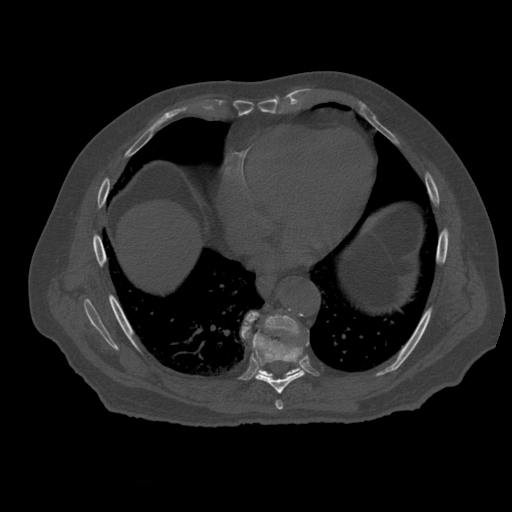
CT including the spine, one axial slice. Slice 335 of 399 in the series (ordered by position). Reconstruction kernel STANDARD. 120 kVp. Bone window (W 1800 / L 400 HU). 1.25 mm slice thickness. 512 × 512 image matrix, field of view 407 × 407 mm. Patient age 73 years. From the clinical record (not read from this slice): primary cancer: prostate.
Structures marked on this image (semi-automatic segmentation, software-assisted and operator-edited):
- T7 vertebra: box from (x=276, y=401) to (x=283, y=410) px
- T8 vertebra: (x=245, y=323)–(x=305, y=394)
- T9 vertebra: (x=242, y=312)–(x=302, y=379)